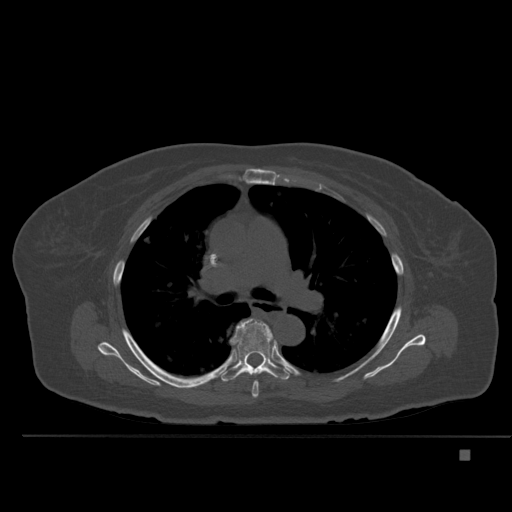
CT including the spine, one axial slice. Slice 344 of 477 in the series (ordered by position). Bone window (W 1800 / L 400 HU). 512 × 512 image matrix, field of view 422 × 422 mm. Patient: female, 74 years. From the clinical record (not read from this slice): primary cancer: colon.
Outlined on this slice (semi-automatic segmentation, software-assisted and operator-edited):
- T5 vertebra: bounding box (x1, y1, x2, y2) in pixels: (252, 381, 259, 399)
- T6 vertebra: (219, 319, 291, 382)